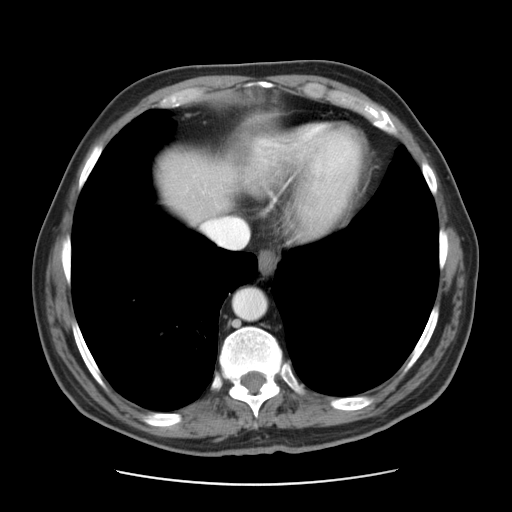
Contrast-enhanced abdominal CT, one axial slice; position 39 of 42 along the scan axis; 120 kVp; intravenous contrast given; soft-tissue window (W 400 / L 40 HU); 5 mm slice thickness; 512 × 512 image matrix. Male patient, age 73 years. From the clinical record (not read from this slice): diagnosis: colorectal cancer liver metastases, imaged before liver resection; multiple liver metastases: yes.
Annotated regions visible in this slice (outlined manually by an expert reader):
- hepatic veins: box from (x=186, y=190) to (x=249, y=249) px
- liver: (x=165, y=157)–(x=231, y=221)
- planned liver remnant (the part of the liver to remain after resection): (x=166, y=158)–(x=231, y=216)